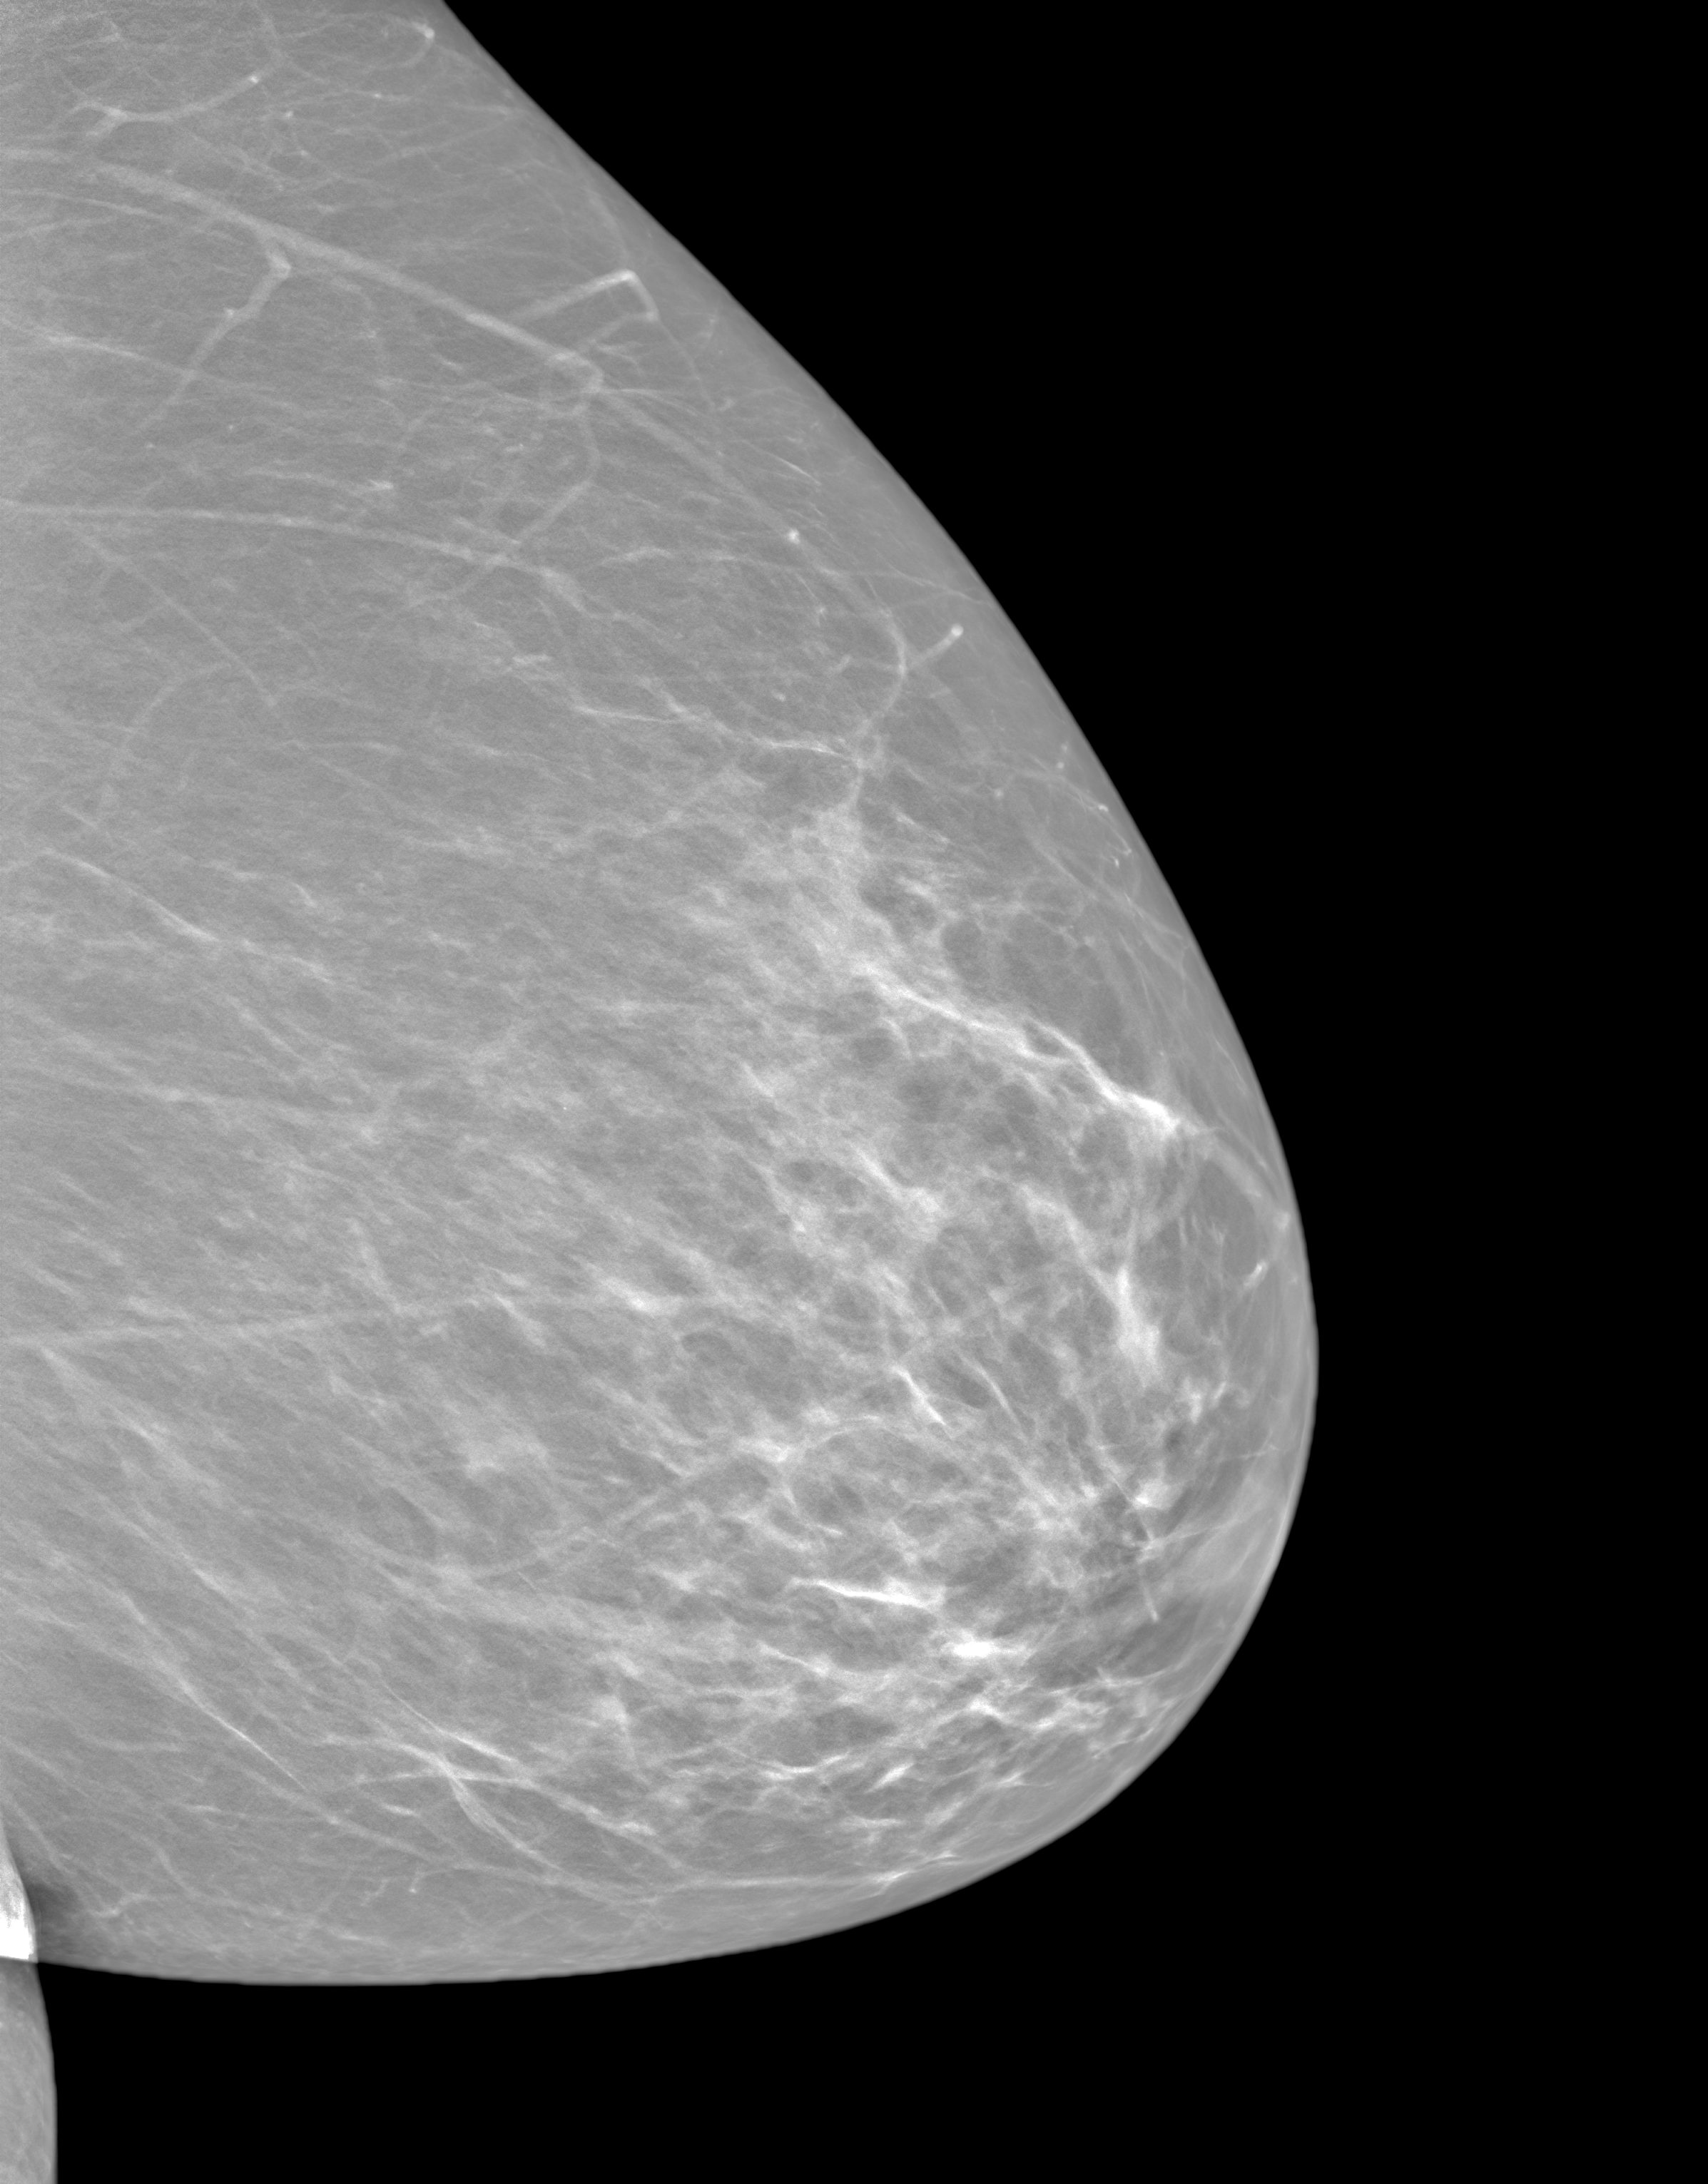
Annual screening mammography examination. Patient aged 58 years (female).
Image type: synthesized 2-D view from tomosynthesis. Breast: left. Projection: mediolateral oblique (MLO) view.